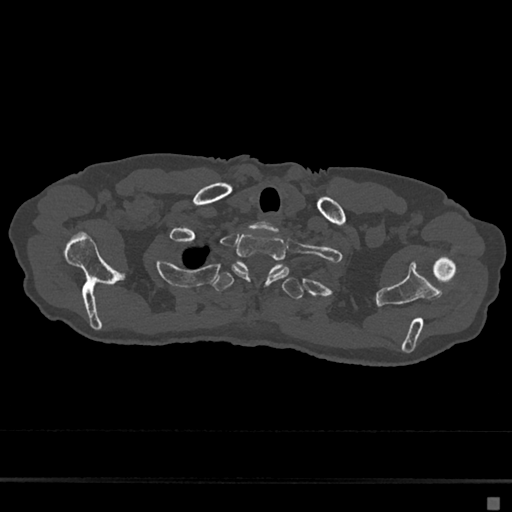
CT including the spine, one axial slice. Slice 598 of 797 in the series (ordered by position). 120 kVp. Bone window (W 1800 / L 400 HU). 0.5 mm slice thickness. 512 × 512 image matrix. Patient: female, 68 years. From the clinical record (not read from this slice): primary cancer: renal.
Outlined on this slice (semi-automatic segmentation, software-assisted and operator-edited):
- T1 vertebra: box from (x=232, y=234) to (x=290, y=283) px
- T2 vertebra: (x=212, y=262)–(x=304, y=299)